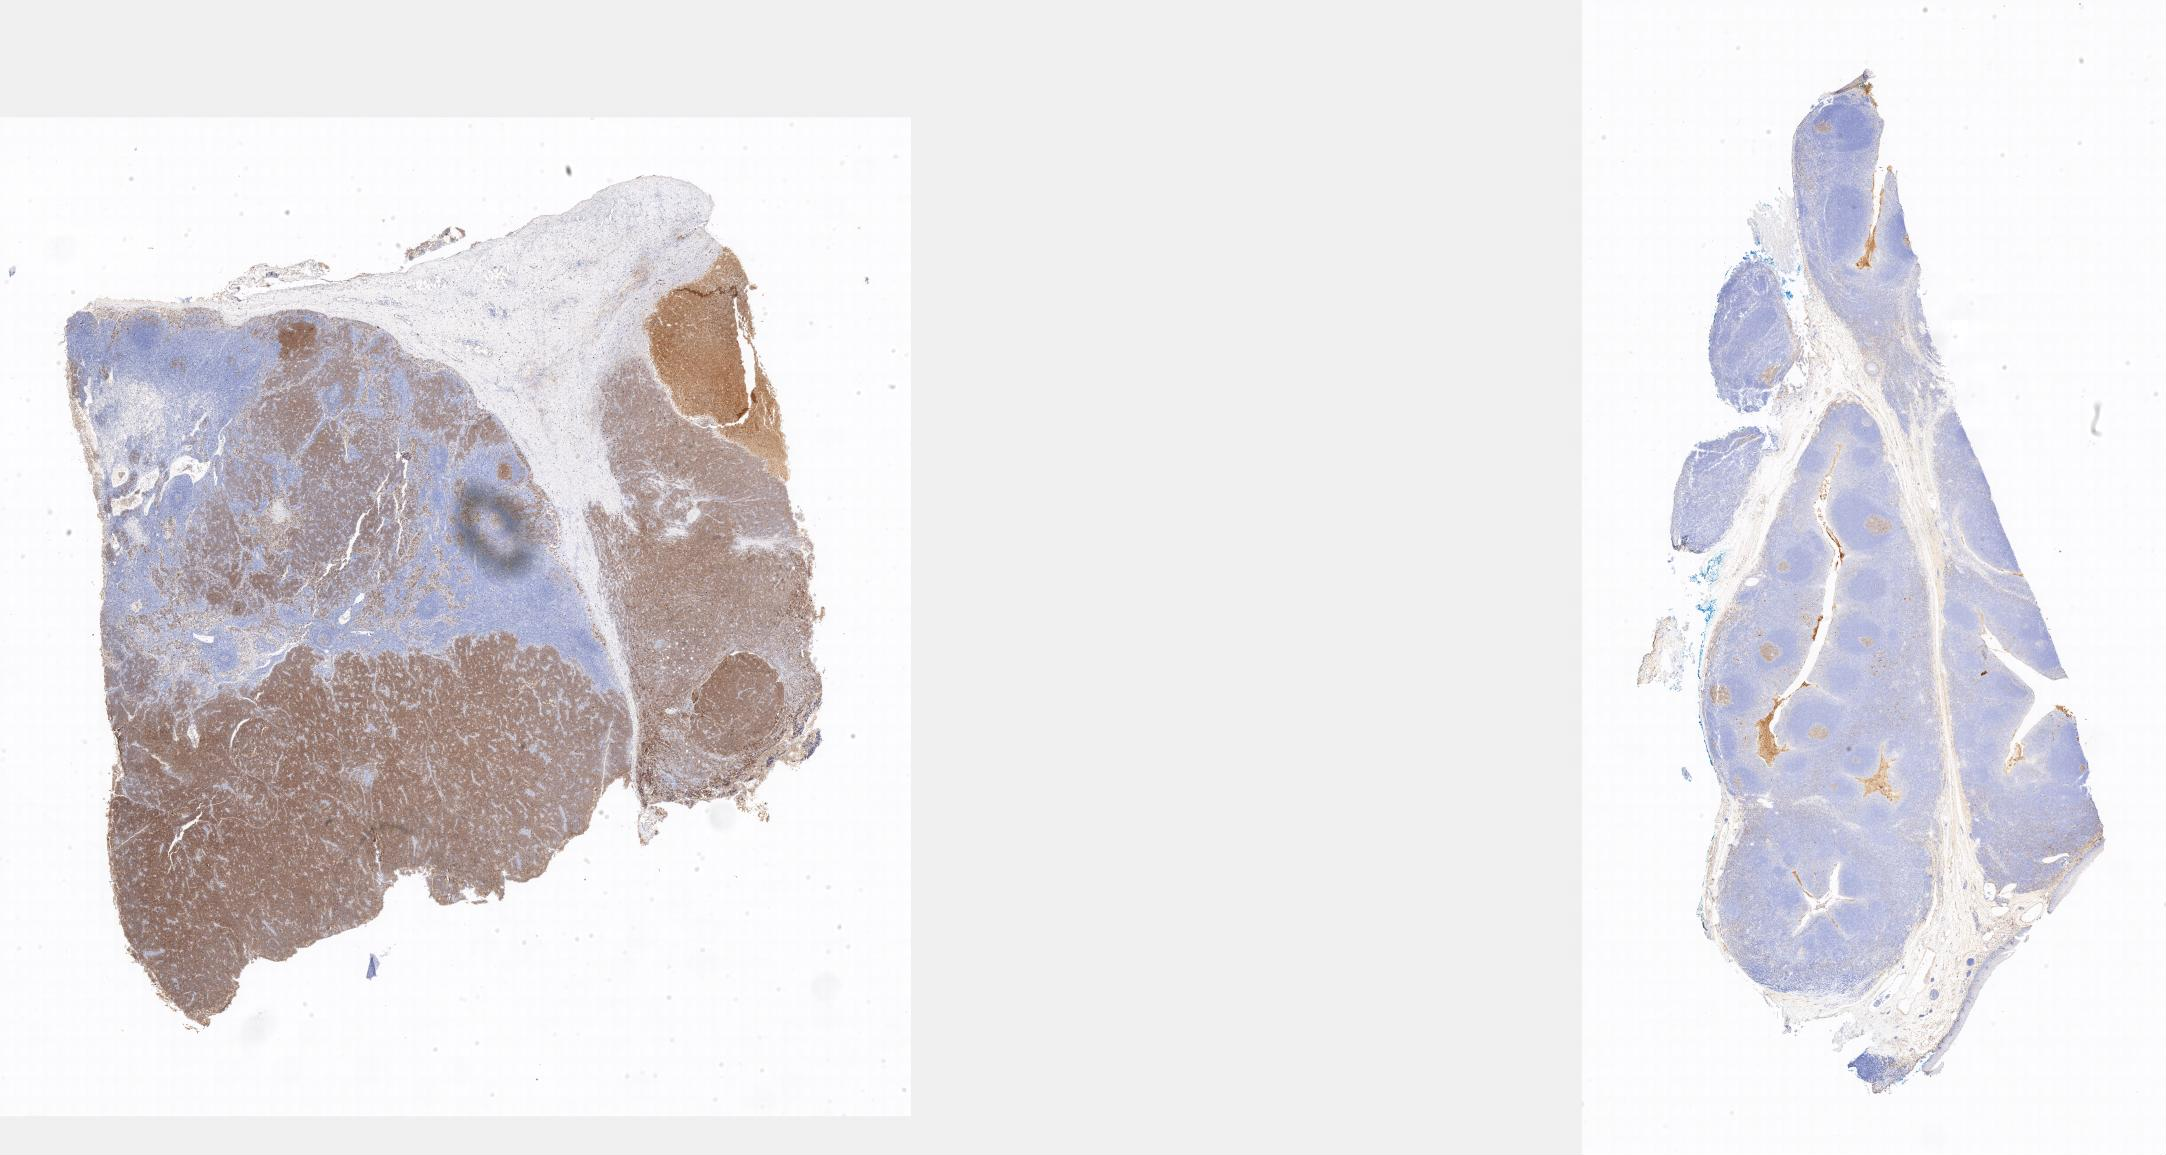
Immunohistochemistry (IHC) whole-slide image stained for CD10, low-resolution overview of the scanned area, specimen: tumor tissue, site: abdominal lymph node. Patient: female, aged 14.
* diagnosis: Burkitt lymphoma, NOS